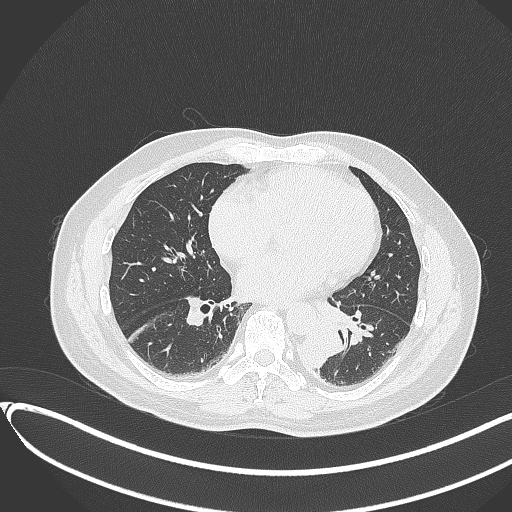
Chest CT, one axial slice; slice 138 of 417 in the series (ordered by position); reconstruction kernel B70f; 120 kVp; lung window (W 1500 / L -600 HU); 512 × 512 image matrix, field of view 400 × 400 mm. Male patient, age 54 years. From the clinical record (not read from this slice): clinical TNM (as recorded): T3 N0 M0.
Structures marked on this image (bounding box drawn by a radiologist):
- lung tumour (recorded histology: squamous cell carcinoma): bounding box (x1, y1, x2, y2) in pixels: (300, 325, 344, 369)